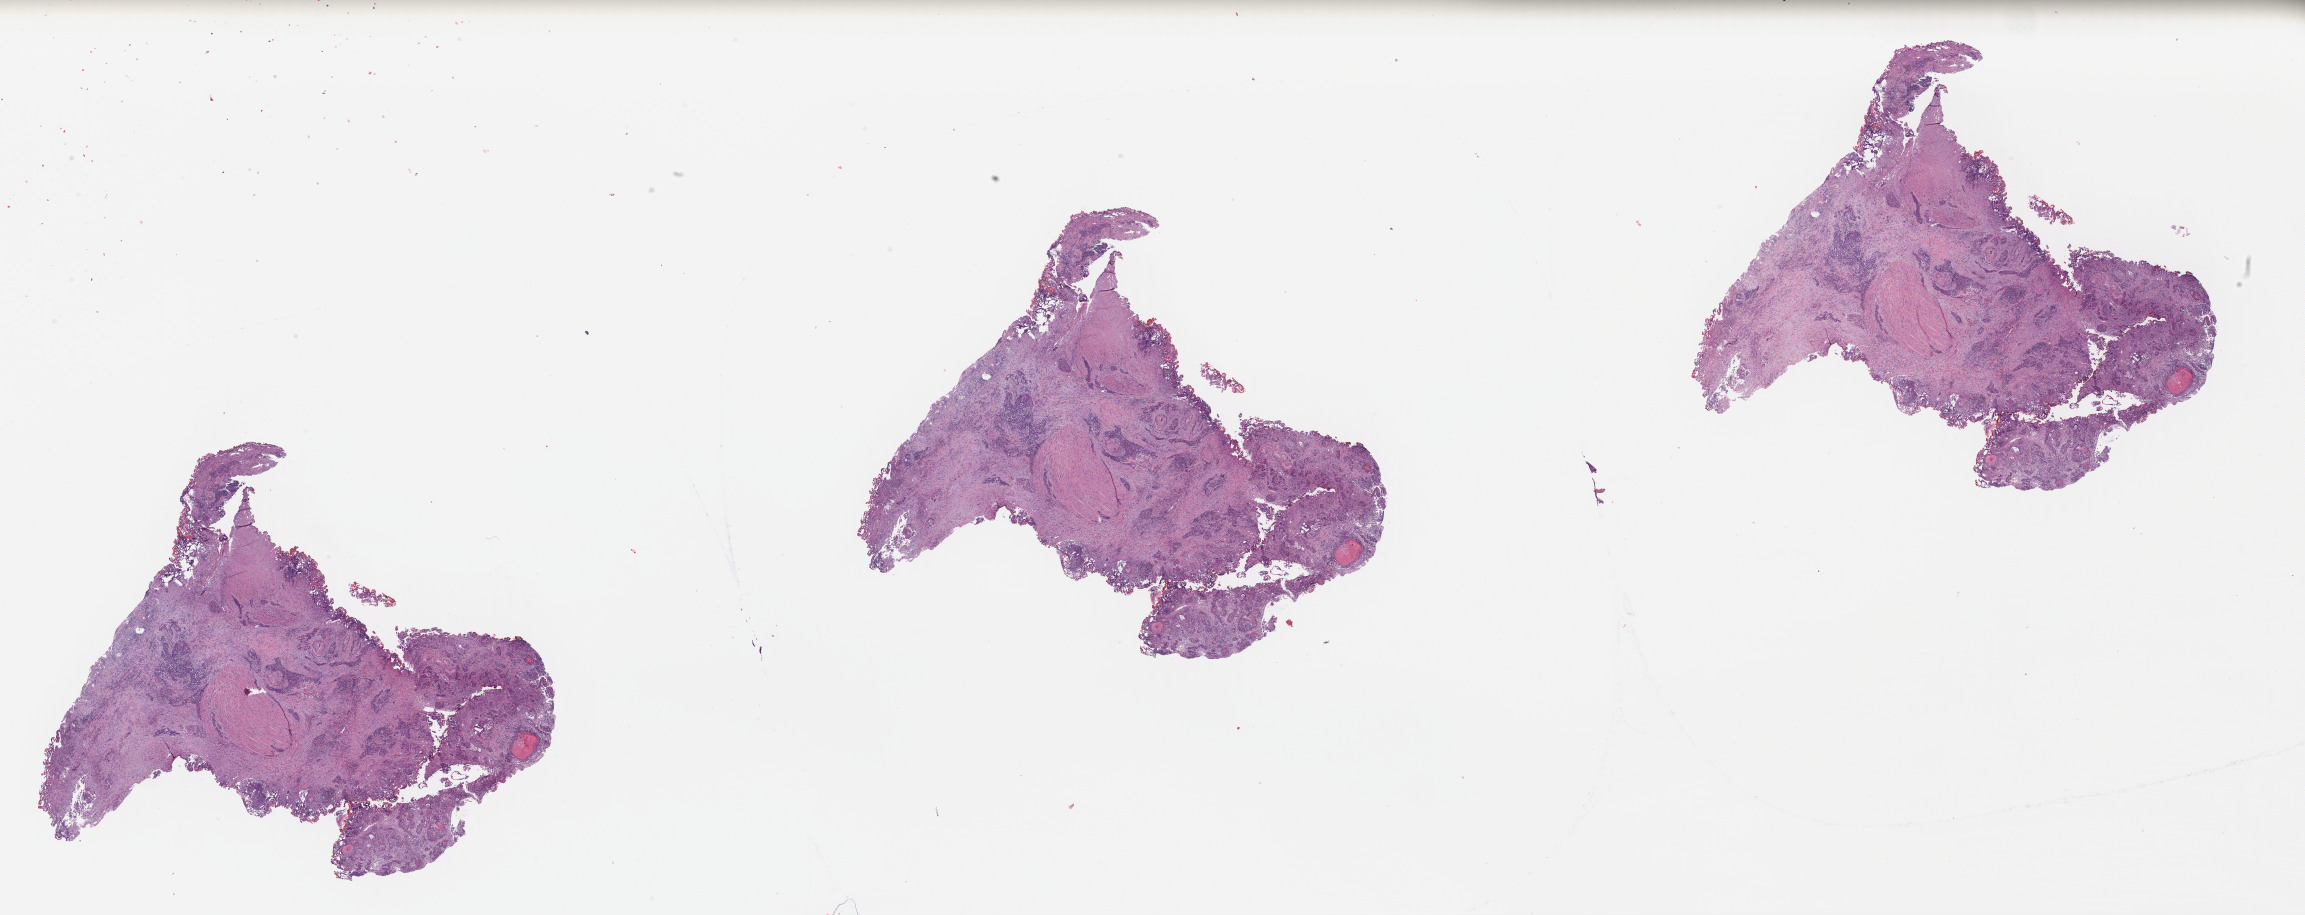
Digitized H&E-stained tissue section (whole slide), shown as a low-resolution overview of the whole scanned area (about 36.2 x 14.4 mm, slide scanned at 40x). Formalin-fixed paraffin-embedded (FFPE) diagnostic section. Primary tumour sample from the bladder. Female, age 54 years at initial diagnosis. Histologic grade: high grade.
Diagnosis: Transitional cell carcinoma. AJCC pathologic stage: II (7th edition).